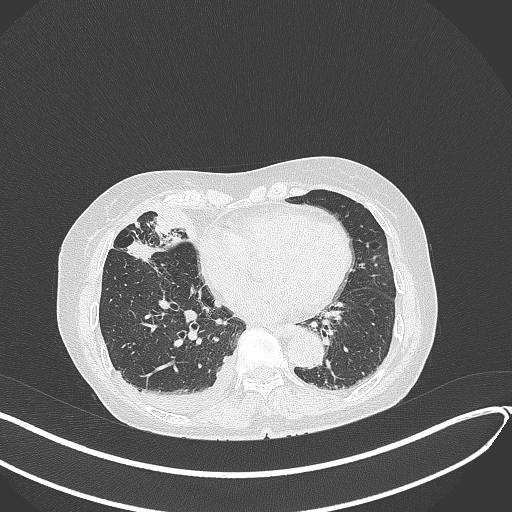
Chest CT, one axial slice. Slice 147 of 418 in the series (ordered by position). 120 kVp. Lung window (W 1500 / L -600 HU). 1 mm slice thickness. 512 × 512 image matrix, field of view 400 × 400 mm. Female patient, age 75 years. Case-level facts recorded for this patient, not image findings: clinical TNM (as recorded): T2a N3 M0.
Outlined on this slice (bounding box drawn by a radiologist):
- lung tumour (recorded histology: adenocarcinoma): box from (x=125, y=239) to (x=159, y=264) px